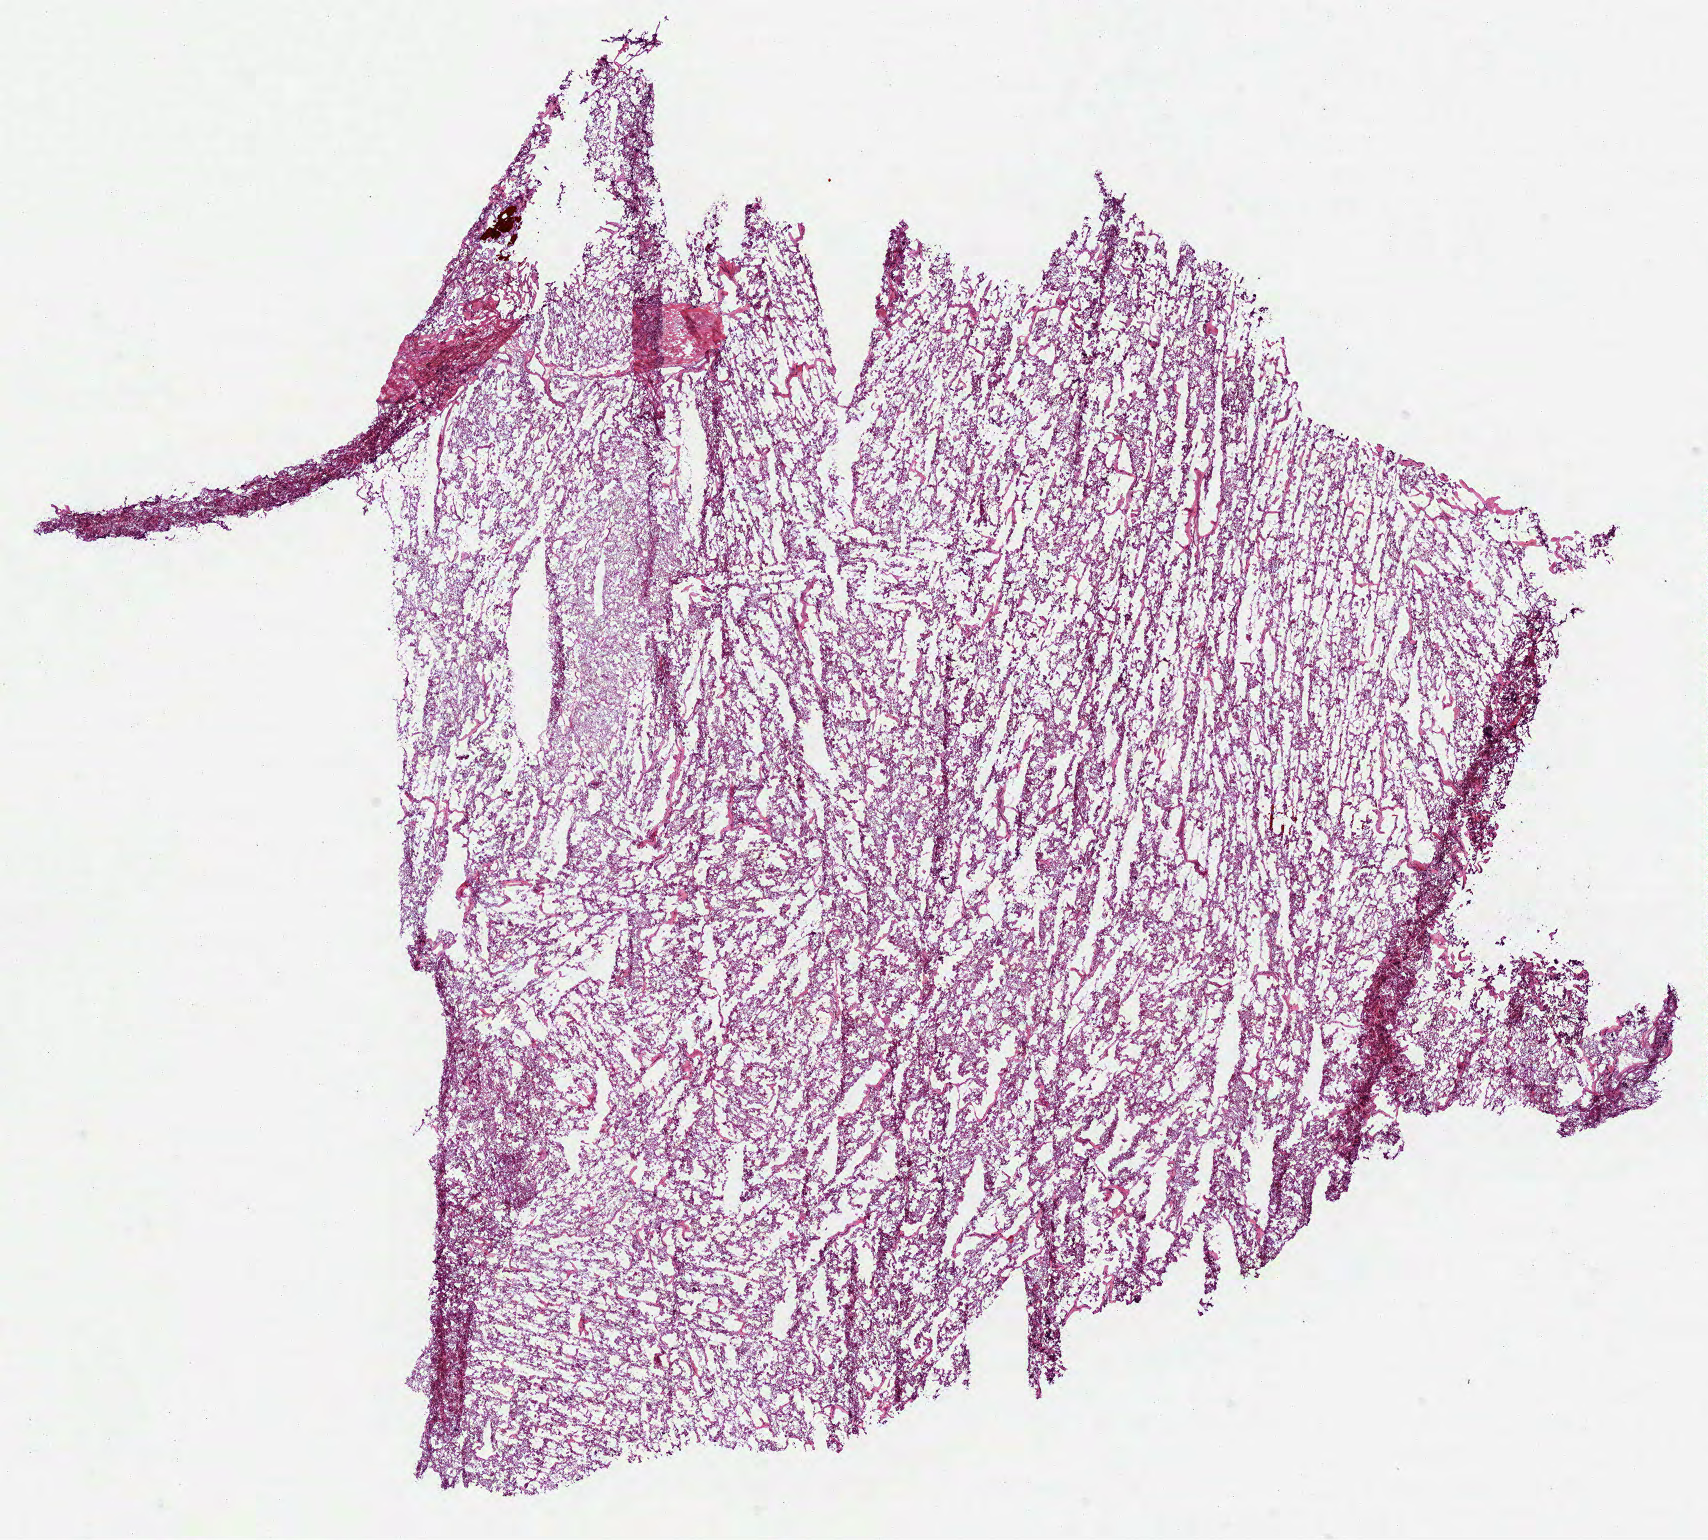
Whole-slide histology image, H&E-stained — shown as a low-resolution overview of the whole scanned area (about 13.8 x 12.4 mm, from a 40x scan); frozen section from the bottom of the tissue portion; sample: primary tumour, kidney. Female patient; age at initial diagnosis 65 years. Pathologist review of this section (percent, as recorded): tumour cells 100%, tumour nuclei 90%, normal cells 0%, stromal cells 0%, necrosis 0%. Infiltration values recorded for this section: lymphocyte infiltration 0%, monocyte infiltration 0%, neutrophil infiltration 0%.
• AJCC pathologic stage: II
• diagnosis: Renal cell carcinoma, chromophobe type